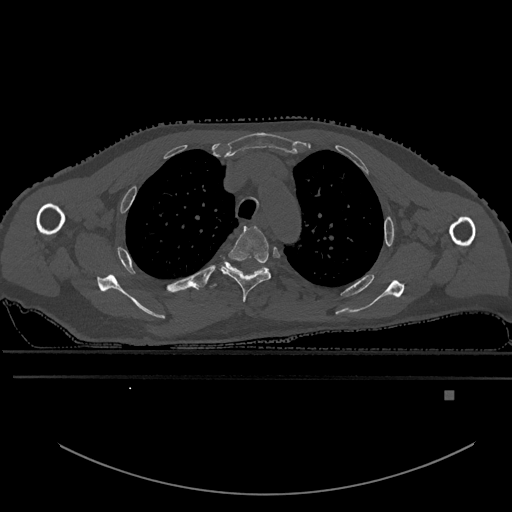
CT including the spine, one axial slice. Slice 443 of 969 in the series (ordered by position). Bone window (W 1800 / L 400 HU). 512 × 512 image matrix. Patient: male, 82 years. Case-level facts recorded for this patient, not image findings: primary cancer: prostate.
Structures marked on this image (semi-automatic segmentation, software-assisted and operator-edited):
- T3 vertebra: bounding box <219,226,272,302> (left, top, right, bottom; pixels)
- T4 vertebra: <209,261,268,289>